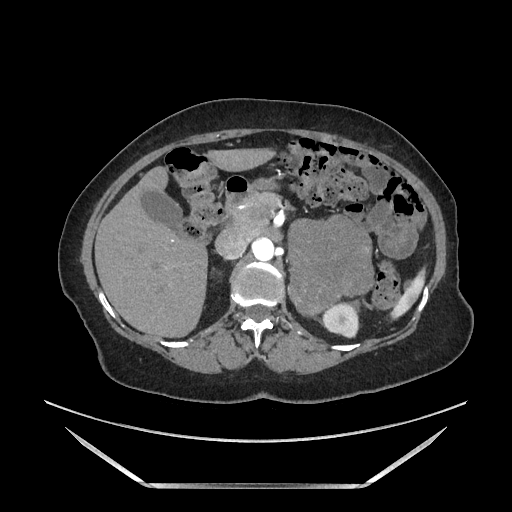
Contrast-enhanced abdominal CT, one axial slice. Position 103 of 205 along the scan axis. Soft-tissue window (W 400 / L 40 HU). 512 × 512 image matrix, field of view 440 × 440 mm. Female patient. Case-level facts recorded for this patient, not image findings: diagnosis: adrenocortical carcinoma; tumour side: left adrenal; tumour size at pathology: 12.5 cm; Ki-67 index: 39 %; stage (as recorded): 3.
Structures marked on this image (semi-automatic segmentation, software-assisted and operator-edited):
- mass: bounding box [x1, y1, x2, y2] px = [290, 219, 373, 315]